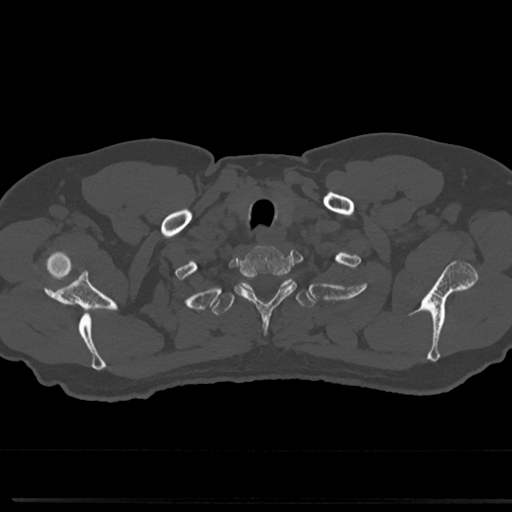
CT including the spine, one axial slice. Slice 660 of 817 in the series (ordered by position). Reconstruction kernel Br40s/3. 120 kVp. Bone window (W 1800 / L 400 HU). 0.5 mm slice thickness. 512 × 512 image matrix. Patient: male, 61 years. From the clinical record (not read from this slice): primary cancer: prostate.
Outlined on this slice (semi-automatically segmented with operator editing):
- T1 vertebra: bounding box [x1, y1, x2, y2] px = [236, 247, 296, 303]
- T2 vertebra: [214, 279, 314, 315]